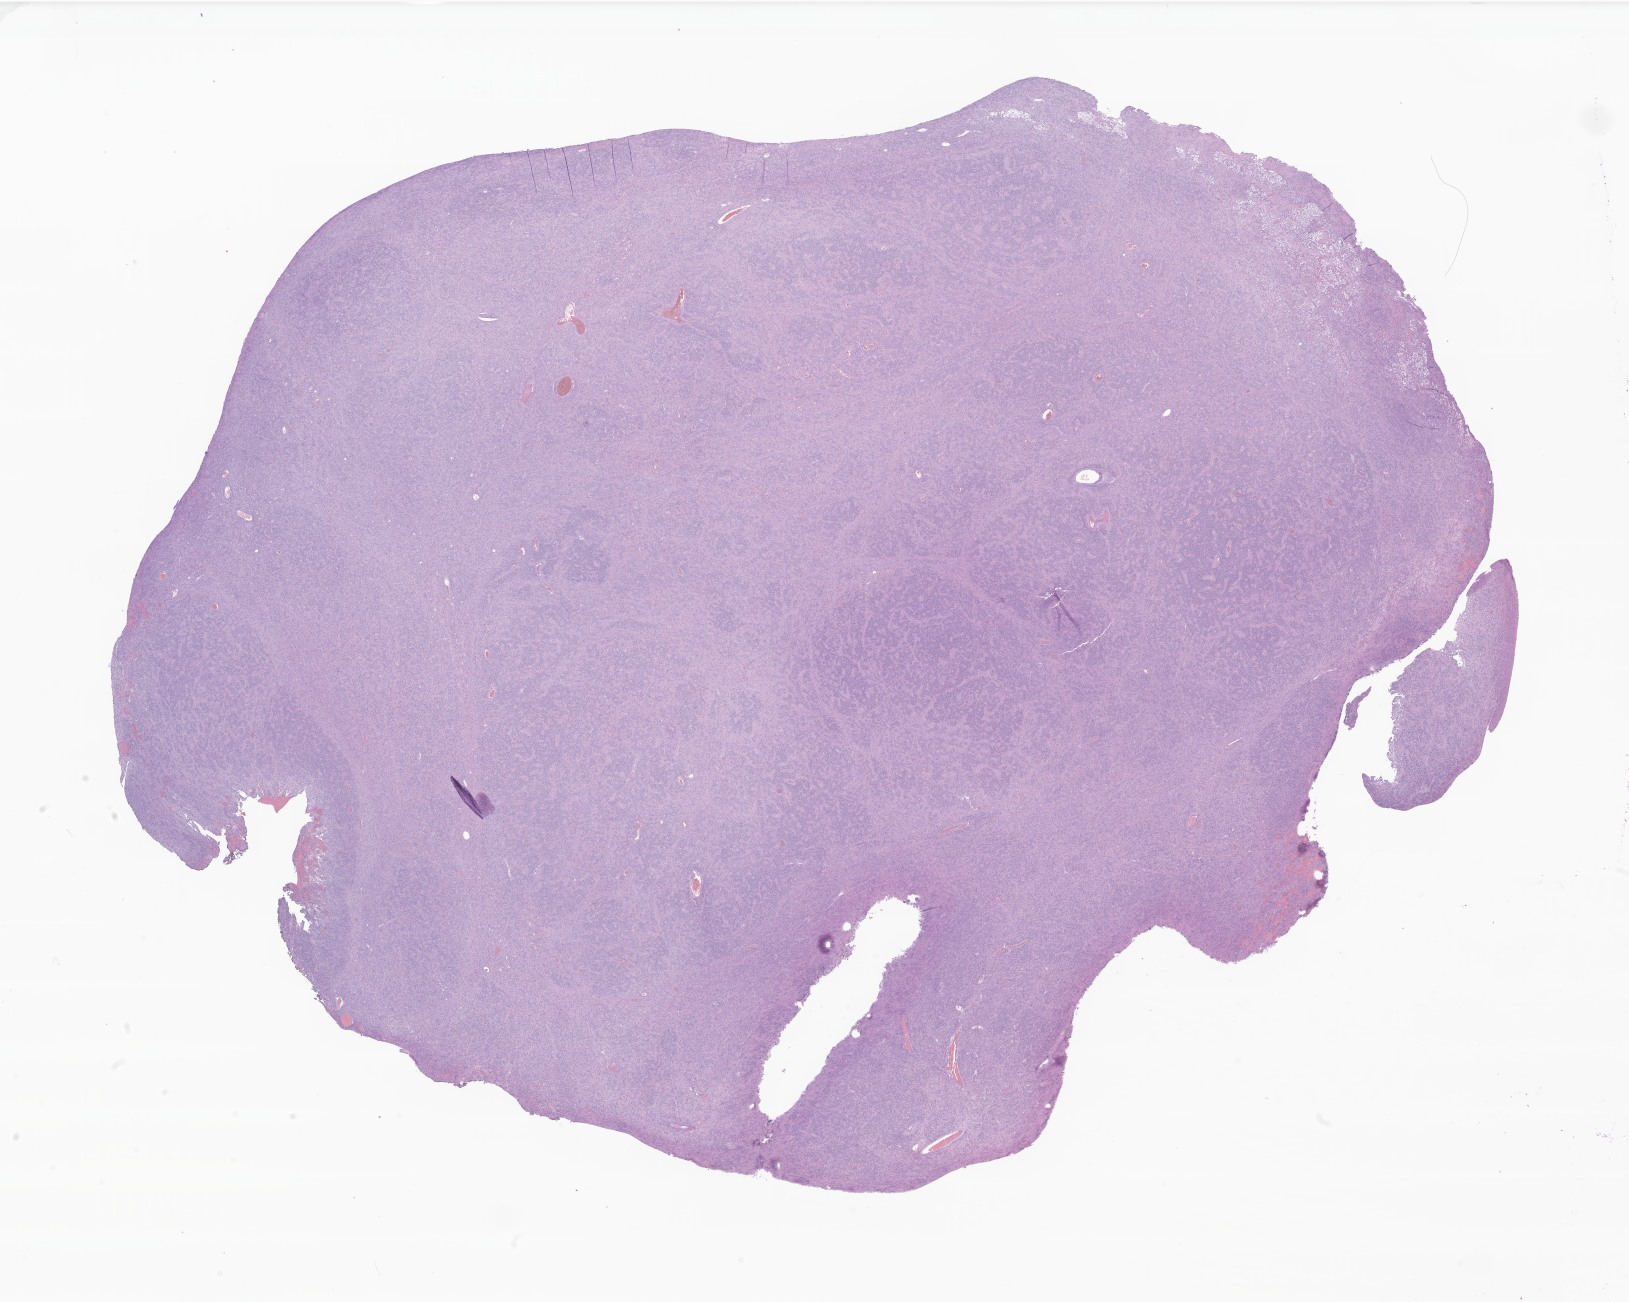
Digitized hematoxylin and eosin (H&E)-stained section of tumor tissue from the brain, whole scanned area (about 27.5 x 22.0 mm) shown as a low-resolution overview. Formalin-fixed, paraffin-embedded (FFPE) tissue. Patient male; age 589 days (about 1.6 years).
Diagnosis: Ependymoma, NOS.